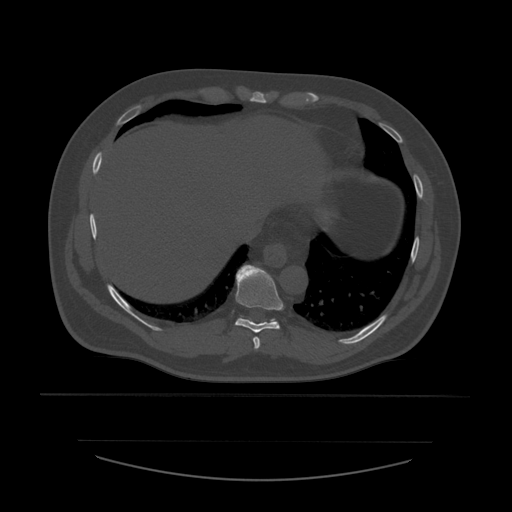
CT including the spine, one axial slice. Position 315 of 532 along the scan axis. 120 kVp. Bone window (W 1800 / L 400 HU). 1.25 mm slice thickness. 512 × 512 image matrix, field of view 441 × 441 mm. Patient age 44 years. From the clinical record (not read from this slice): primary cancer: soft tissue sarcoma.
Structures marked on this image (semi-automatically segmented with operator editing):
- T10 vertebra: bounding box <240,318,275,320> (left, top, right, bottom; pixels)
- T8 vertebra: <253,337,261,350>
- T9 vertebra: <235,265,283,333>